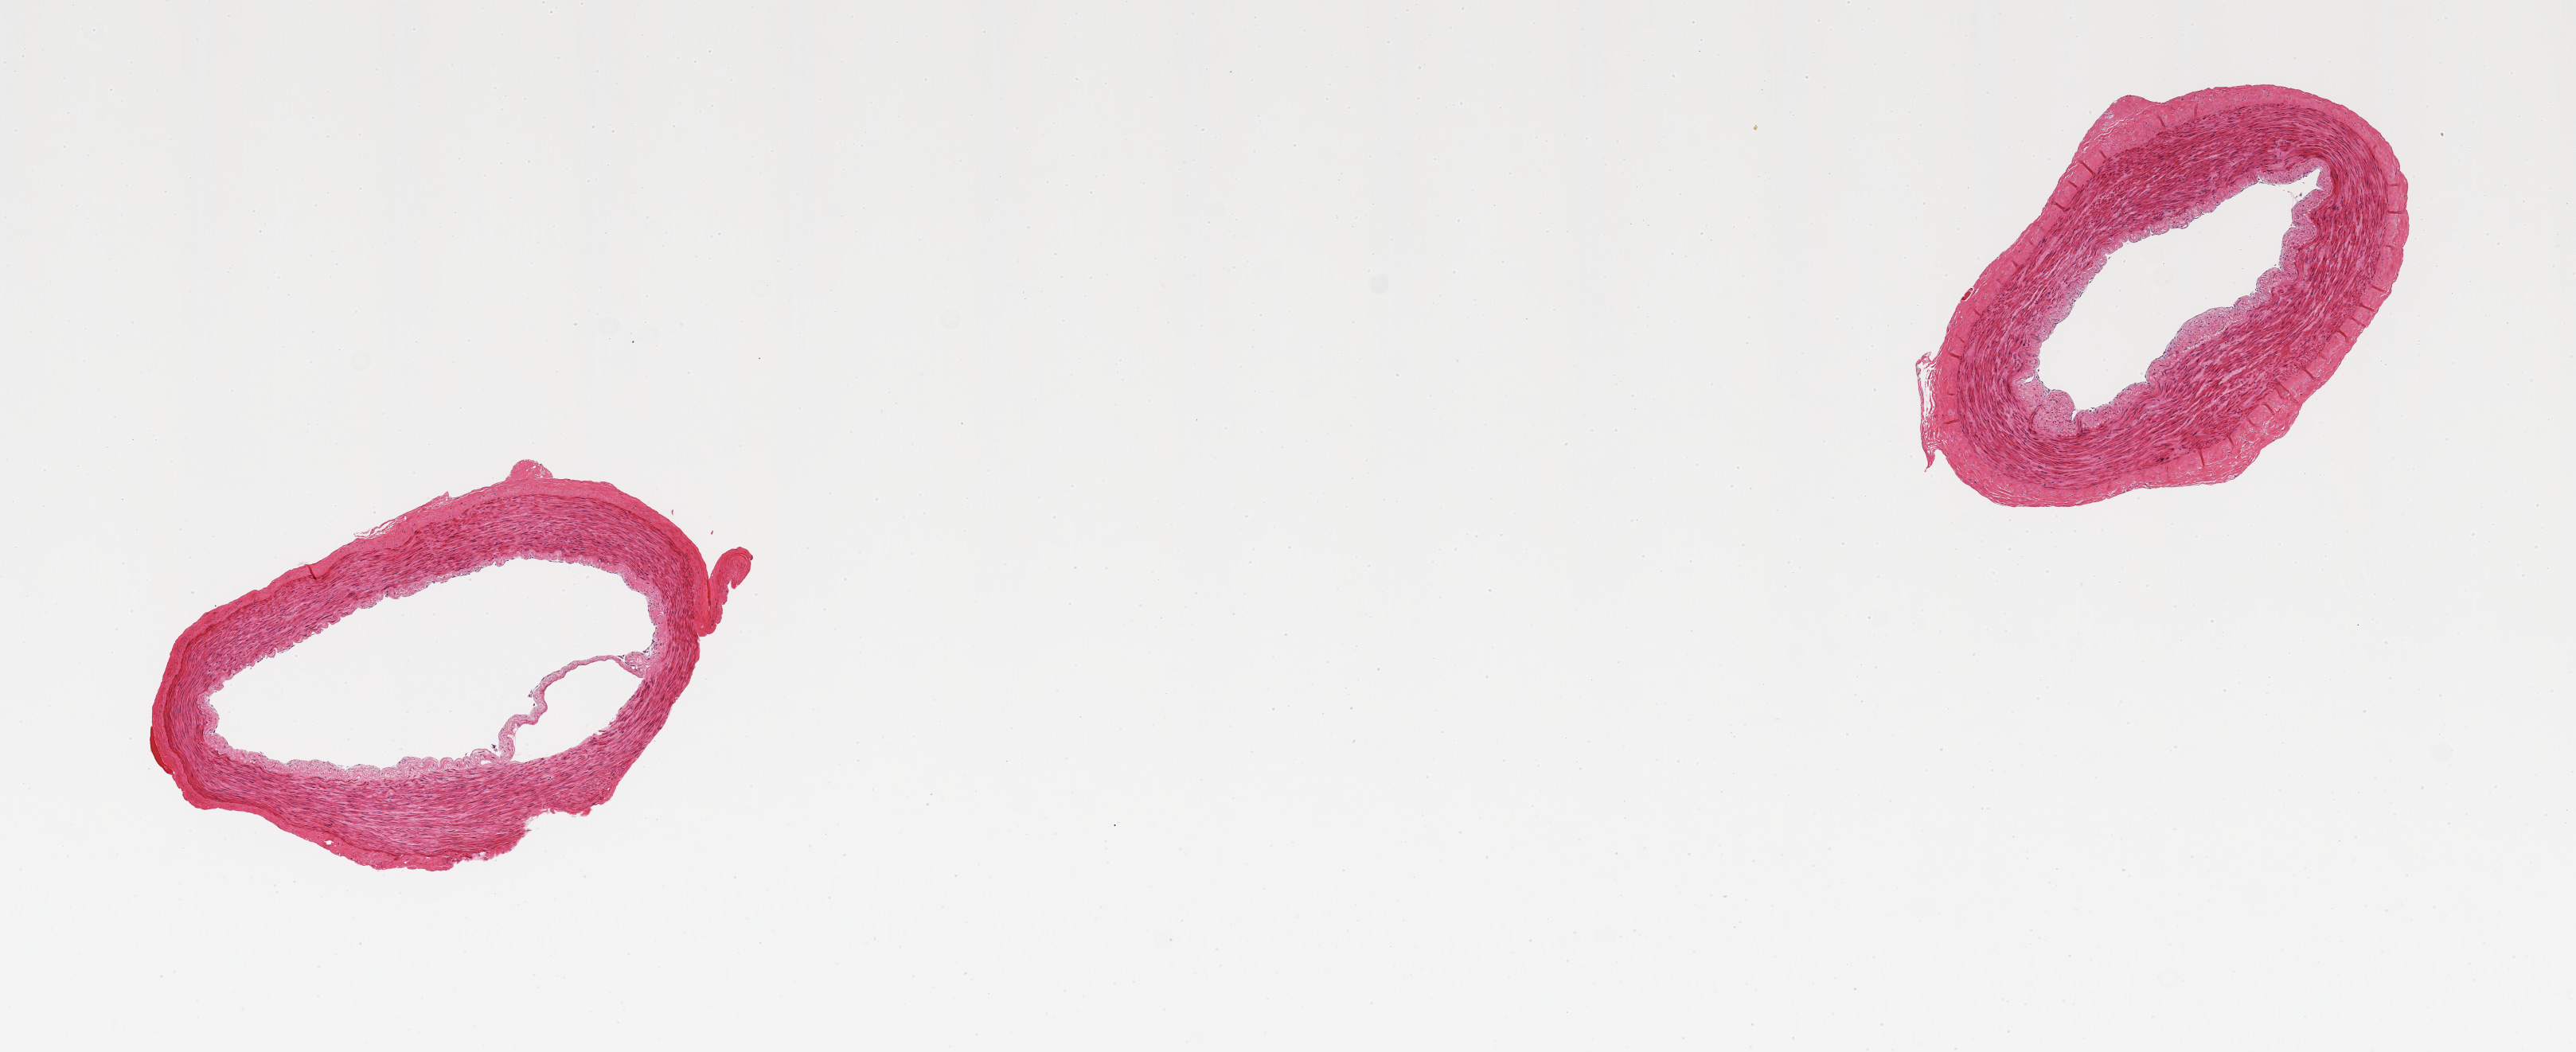
Haematoxylin and eosin whole-slide image — a low-resolution overview of the entire scanned area, about 12.8 x 5.2 mm, PAXgene-fixed, paraffin-embedded tissue, target tissue: tibial artery, tissue donor sample. Donor: male.
* pathologist's review note for this sample: 2 pieces; not nerve, cross sections of artery with small rim of adventitia; lumen open